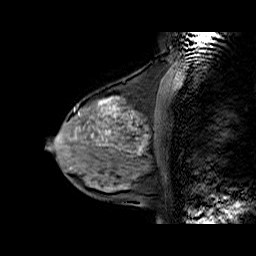
Breast MRI (dynamic contrast-enhanced), one sagittal slice; position 24 of 60 along the scan axis; dynamic contrast-enhanced series, time point 2 of 6 at this slice position (early post-contrast); 1.5 T; TE 6.3 ms, TR 32.9 ms; 4 mm slice thickness; 256 × 256 image matrix, field of view 200 × 200 mm. Female patient. From the clinical record (not read from this slice): setting: breast cancer imaged before/during neoadjuvant chemotherapy; receptor status: HR-positive, HER2-negative.
Structures marked on this image (semi-automatically segmented with operator editing):
- analysis volume of interest (the breast-tissue region the enhancement analysis was run in; not a lesion): bounding box (x1, y1, x2, y2) in pixels: (57, 86, 169, 170)
- tumour enhancement mask (voxels above the 100 % enhancement threshold inside the analysis volume of interest): (98, 97, 118, 133)